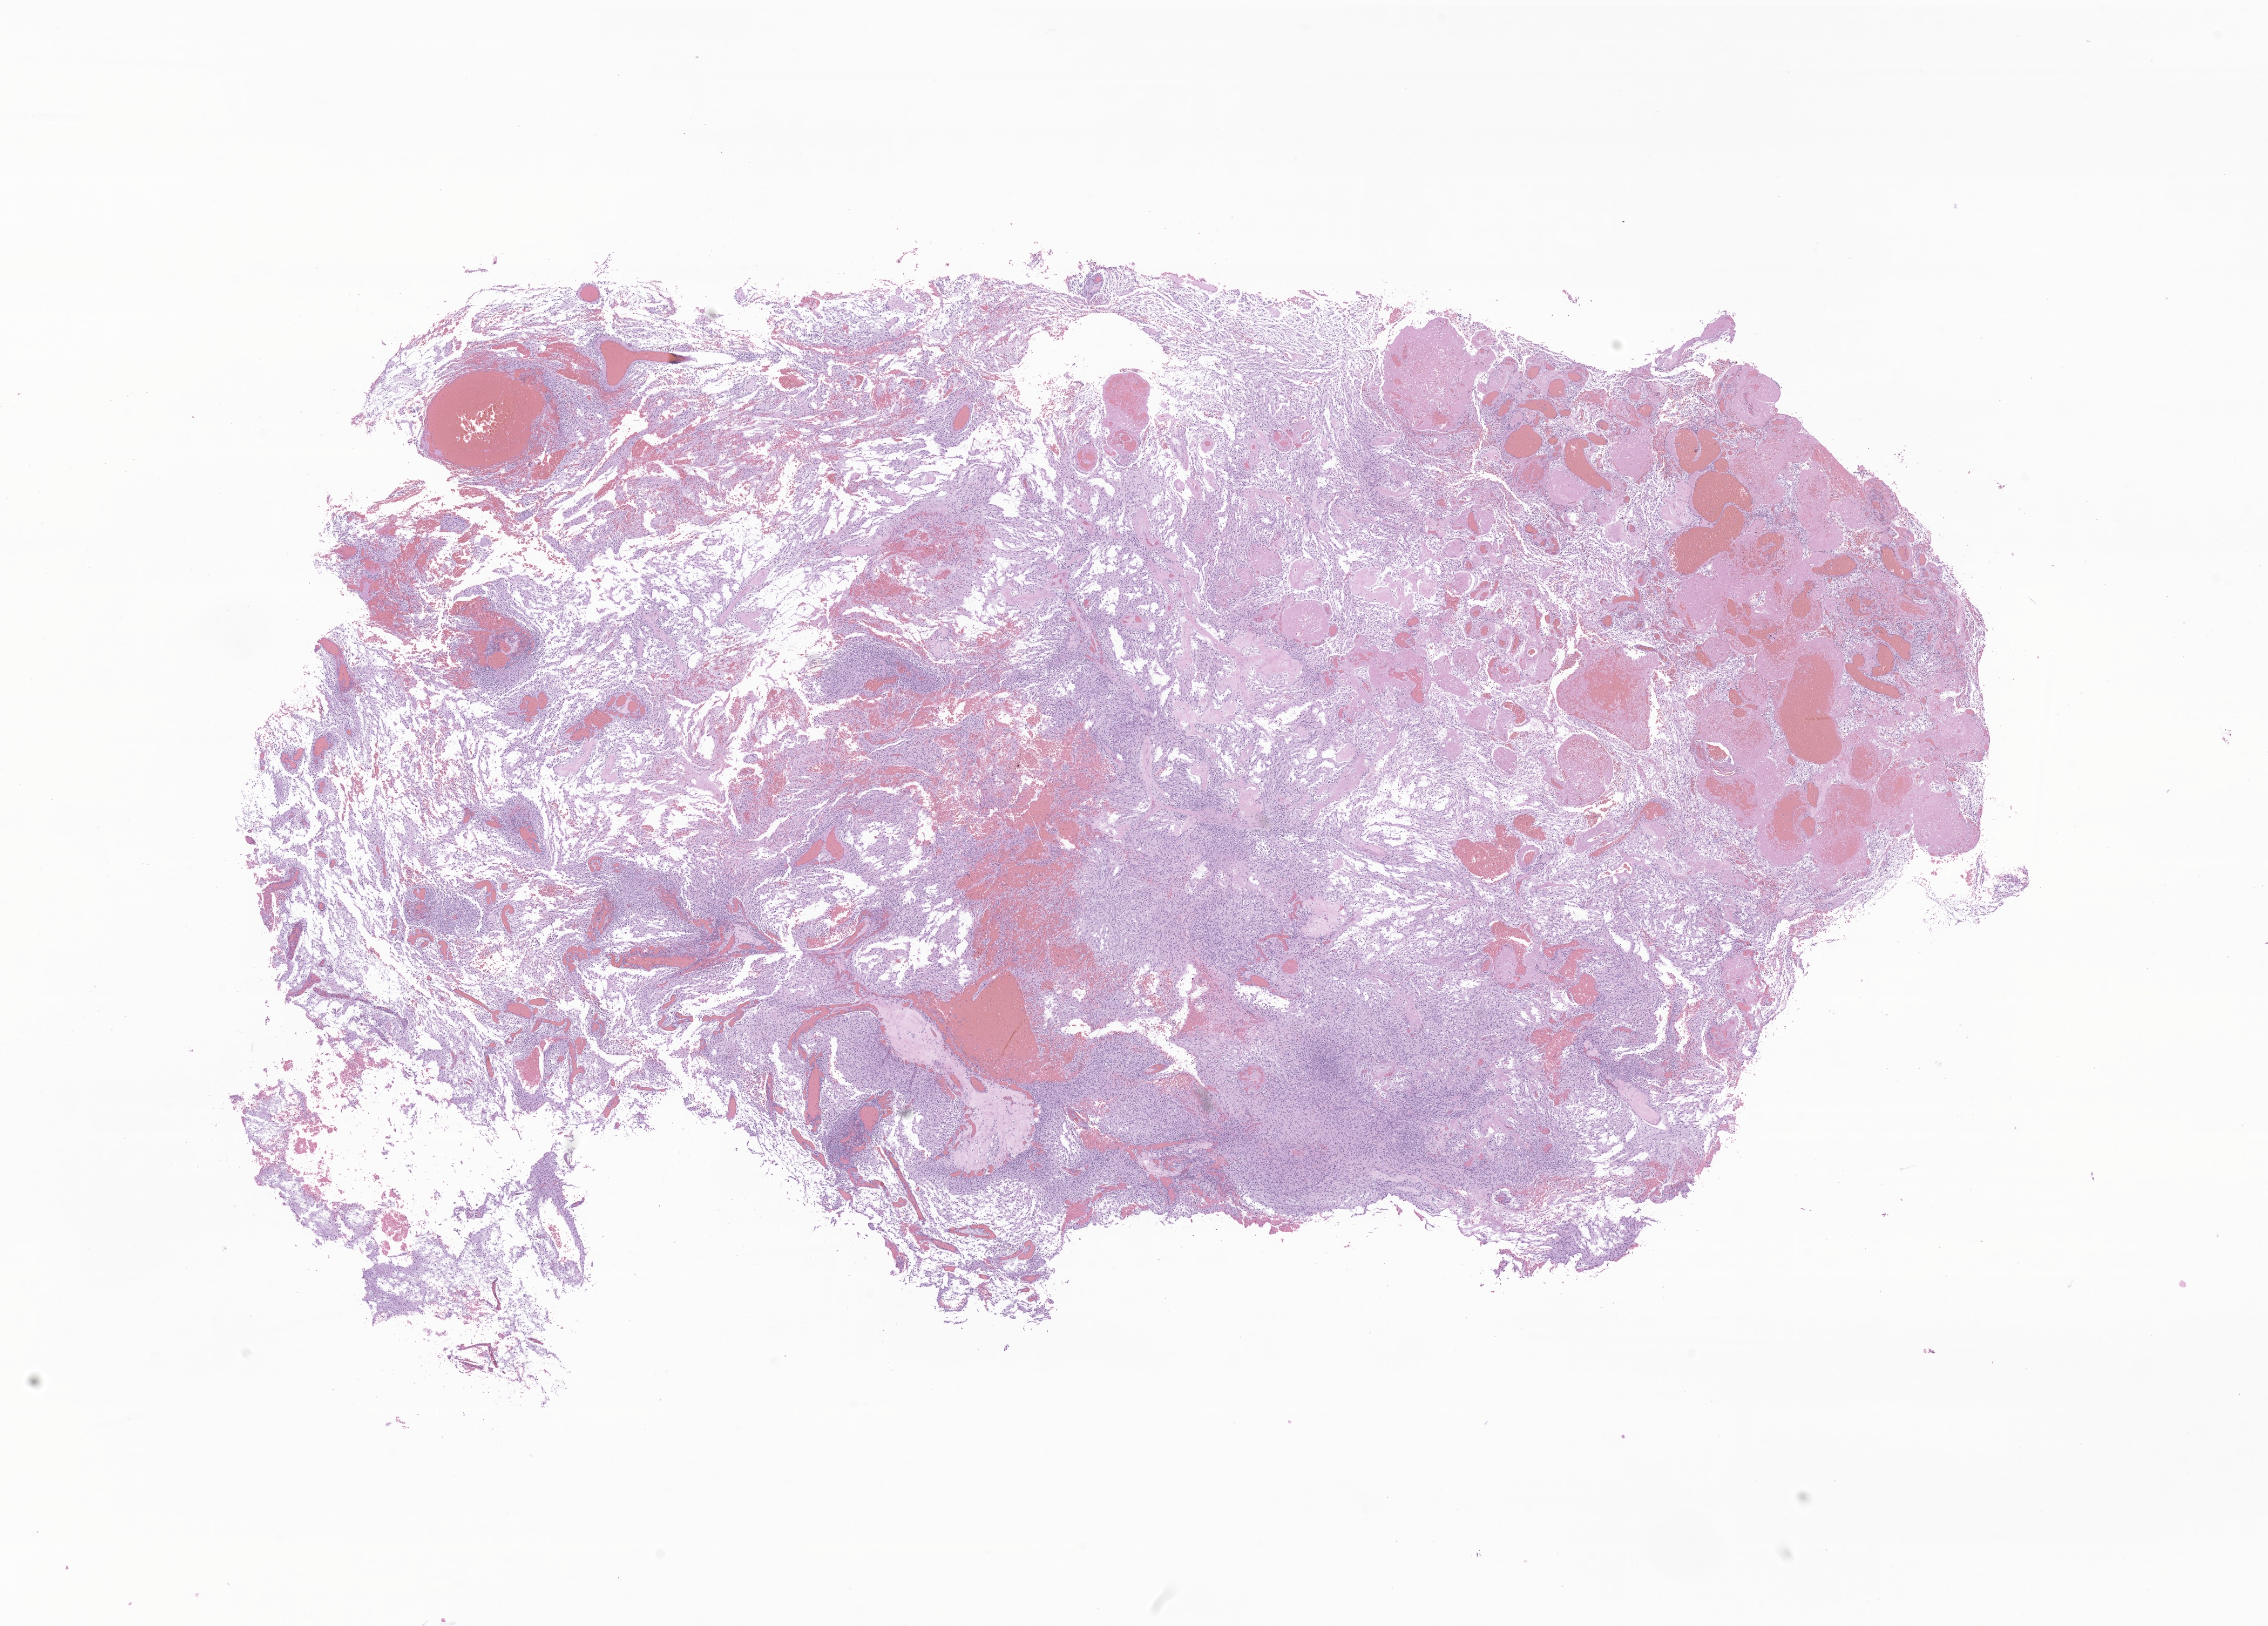
Hematoxylin and eosin (H&E) whole-slide image of tumor tissue from the frontal lobe, a low-resolution overview of the entire scanned area, about 17.7 x 12.7 mm, FFPE section. Patient male; age 122 months (10 years 2 months).
Diagnosis: Glioma, malignant.